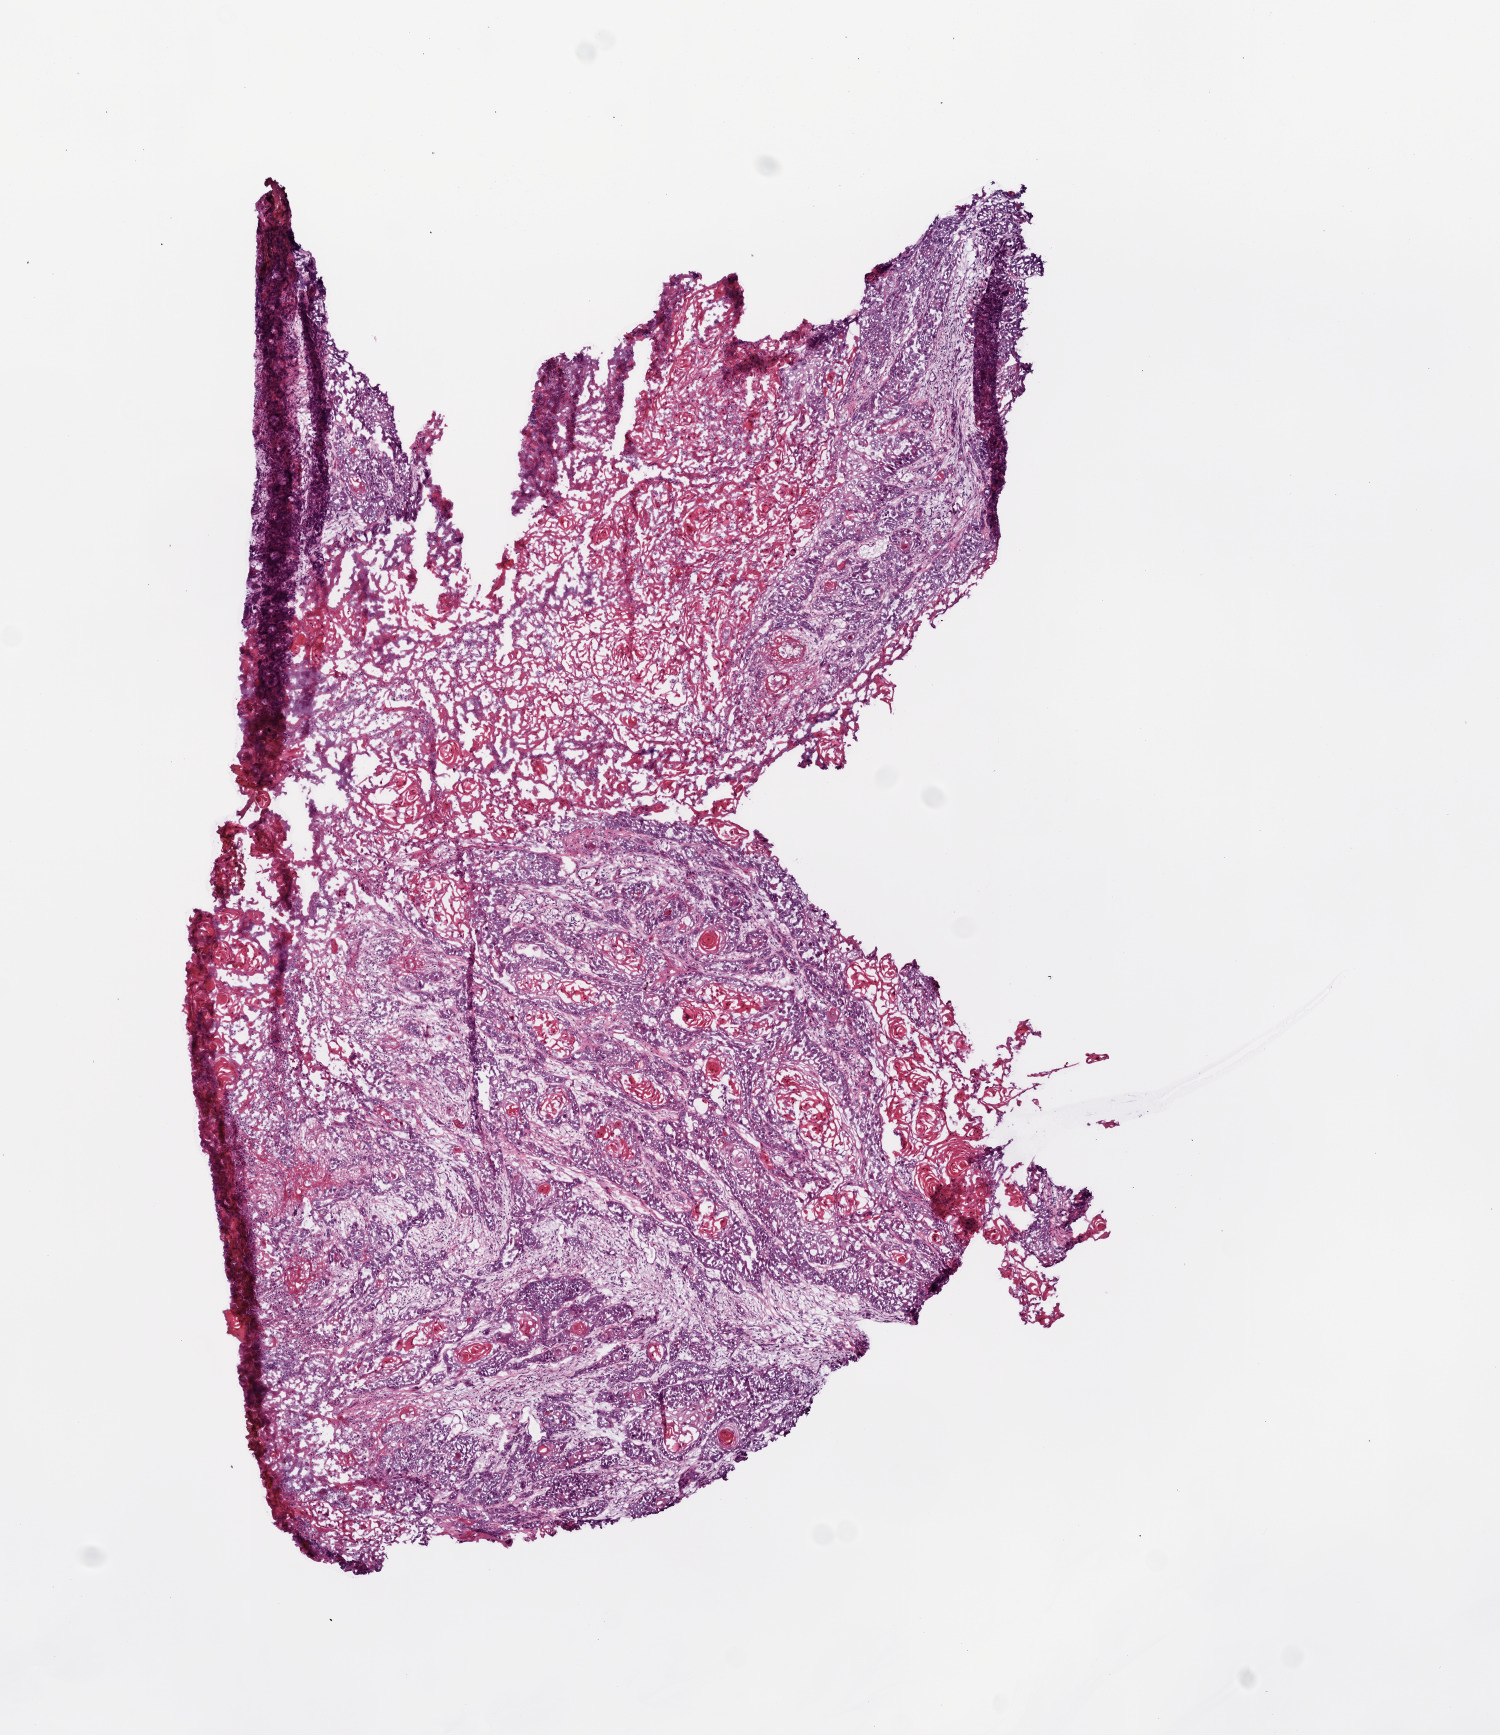
Digitized H&E tissue section (whole slide) — whole scanned area (about 6.0 x 7.0 mm, slide scanned at 20x) shown as a low-resolution overview; frozen section from the top of the tissue portion; sample: primary tumour, head and neck. Male, age 67 years at initial diagnosis. Histologic grade: G3 (poorly differentiated). Slide review estimates, as recorded: tumour cells 65%, tumour nuclei 75%, normal cells 0%, stromal cells 15%, necrosis 20%.
* TNM: T4a N2c
* histologic diagnosis: Squamous cell carcinoma, NOS (overlapping lesion of lip, oral cavity and pharynx)
* AJCC pathologic stage: IVA (6th edition)